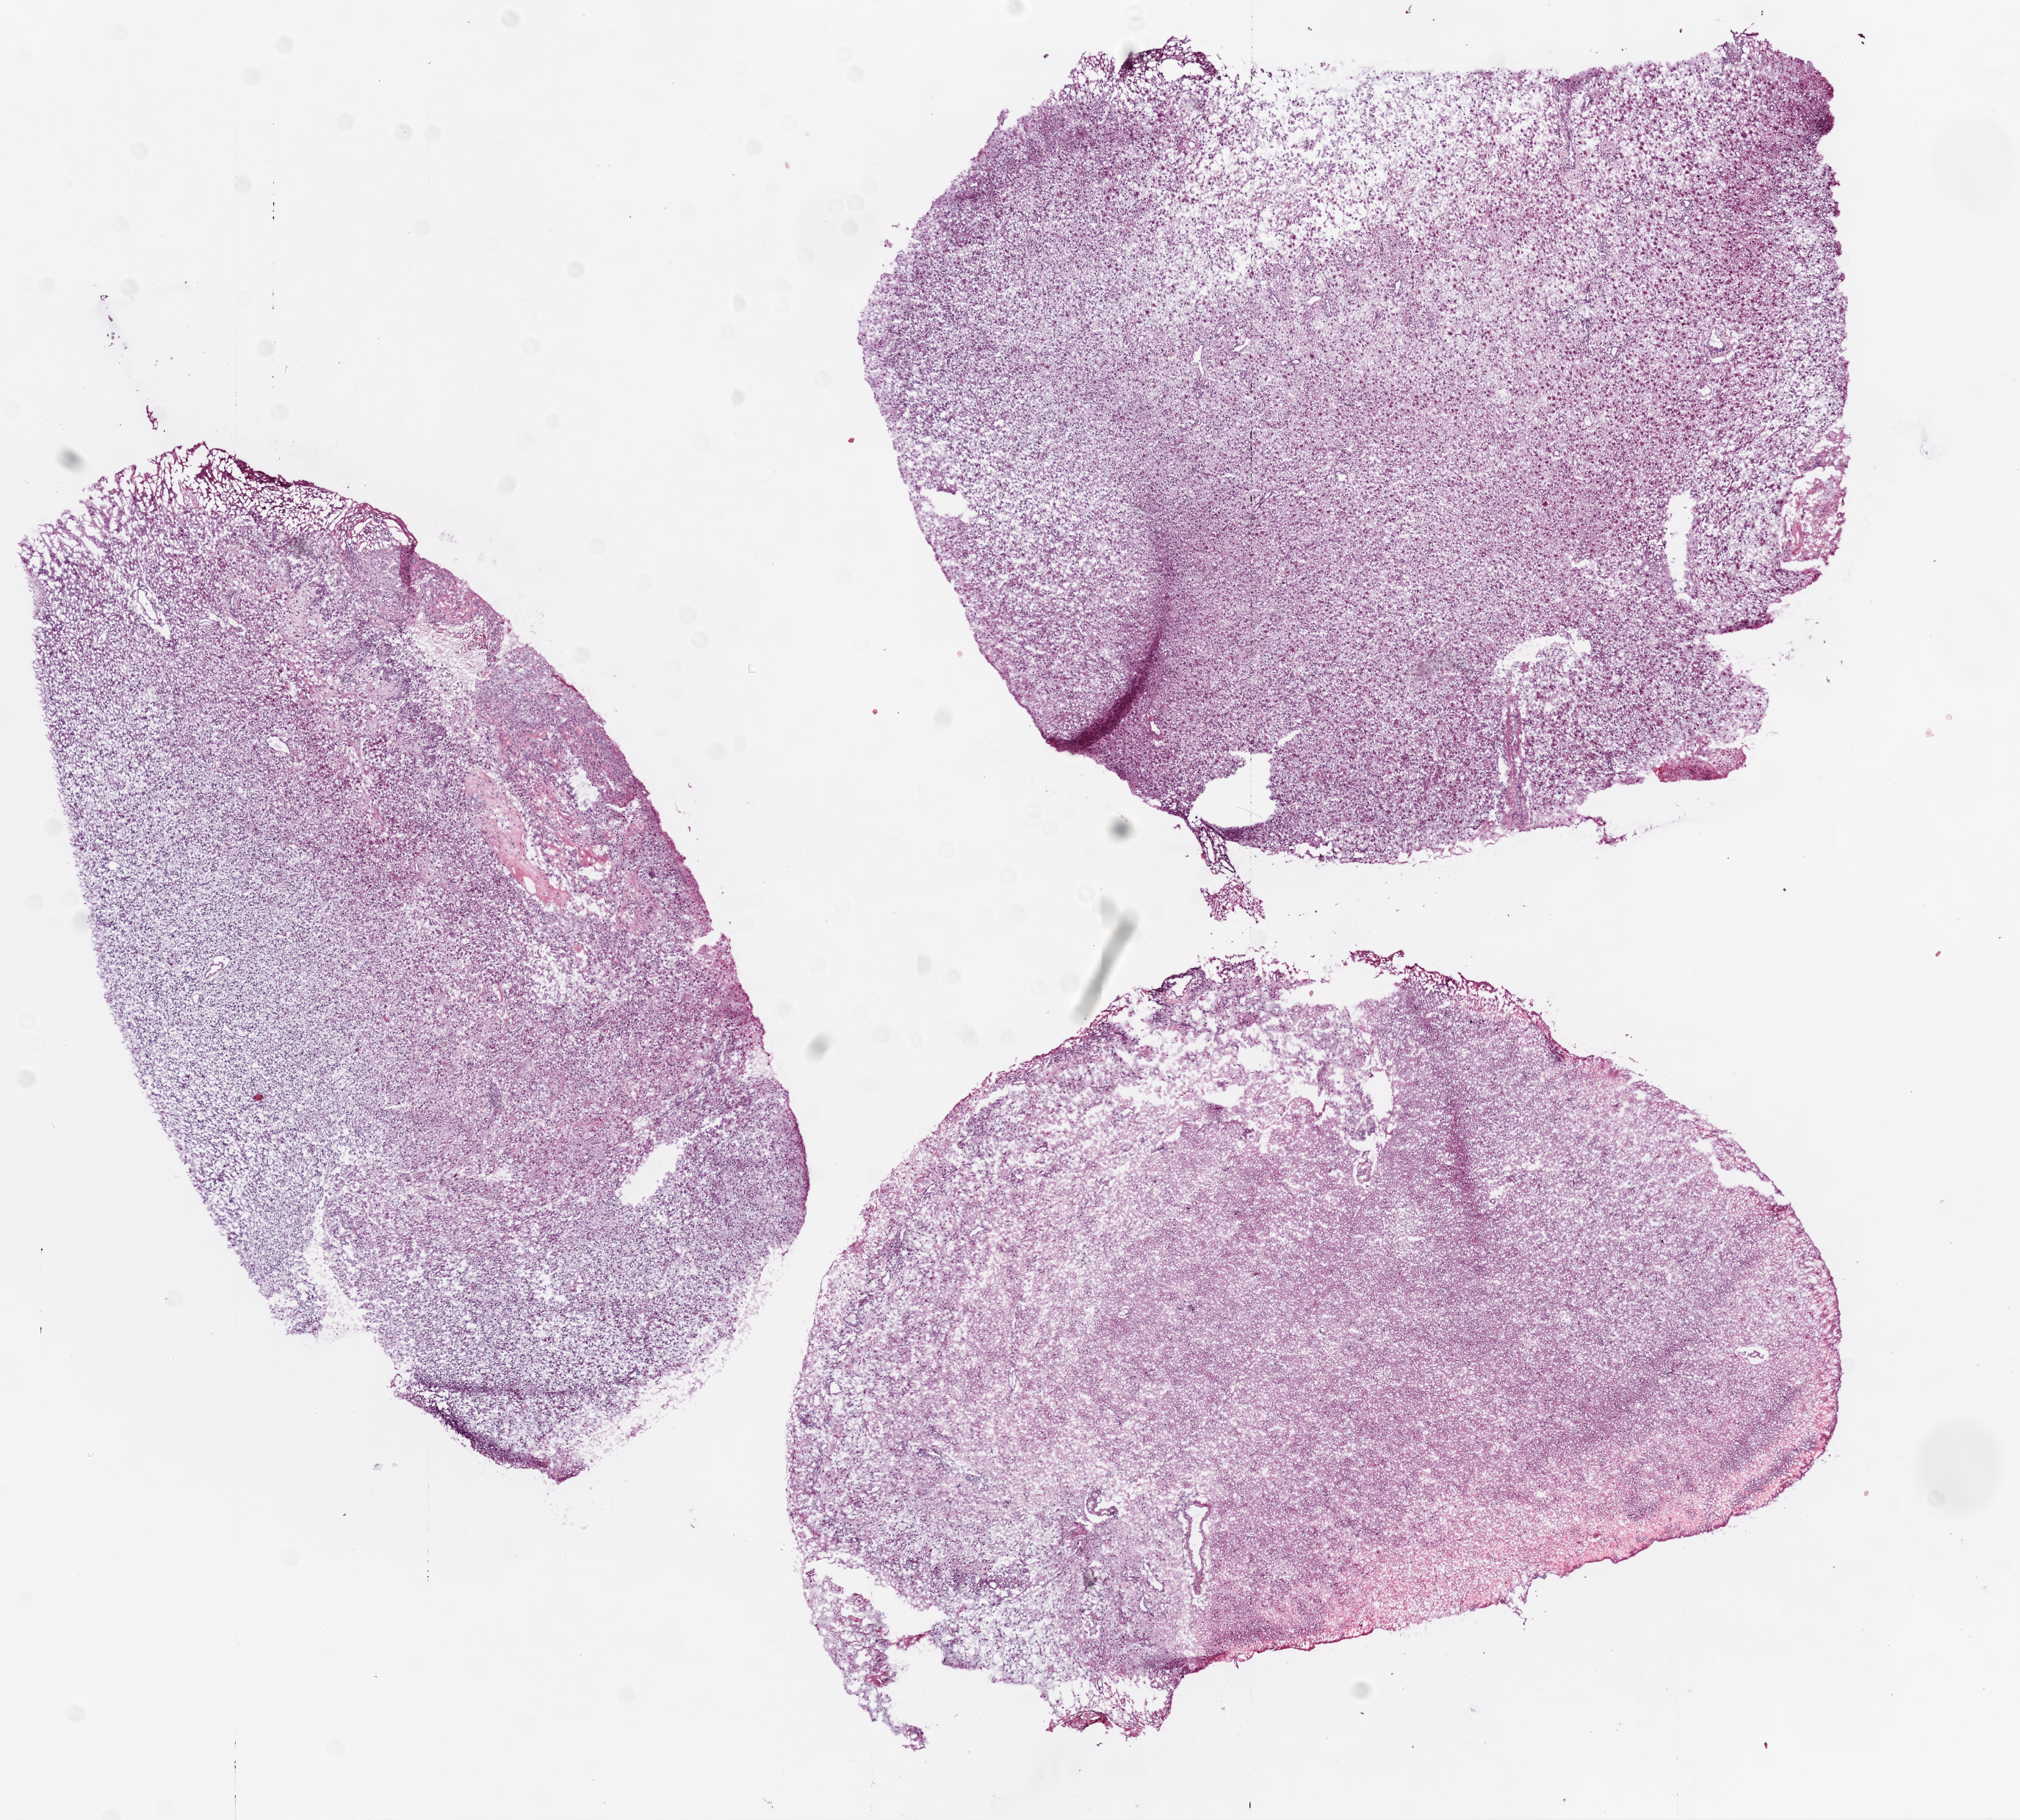
Digitized H&E-stained tissue section (whole slide), whole scanned area (about 11.0 x 9.9 mm, from a 20x scan) shown as a low-resolution overview. Frozen section from the bottom of the tissue portion. Sample: primary tumour, brain. Male, age 57 years at initial diagnosis. Composition of this section per pathologist review: tumour cells 80%, tumour nuclei 80%, normal cells 15%, stromal cells 5%, necrosis 0%.
Histologic diagnosis: Glioblastoma.